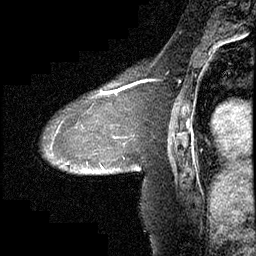
Breast MRI (dynamic contrast-enhanced), one sagittal slice; slice 140 of 232 in the series (ordered by position); dynamic contrast-enhanced study with each time point stored as its own series, time point 2 of 4 at this slice position (early post-contrast, ordered by acquisition time); 1.5 T; TE 4.2 ms, TR 6.7 ms; 256 × 256 image matrix, field of view 200 × 200 mm. Patient: female, 63 years. From the clinical record (not read from this slice): setting: breast cancer imaged before/during neoadjuvant chemotherapy; receptor status: triple-negative.
Outlined on this slice (semi-automatic segmentation, software-assisted and operator-edited):
- analysis volume of interest (the breast-tissue region the enhancement analysis was run in; not a lesion): bounding box (x1, y1, x2, y2) in pixels: (43, 90, 140, 175)
- tumour enhancement mask (voxels above the 70 % enhancement threshold inside the analysis volume of interest): (100, 90, 120, 171)